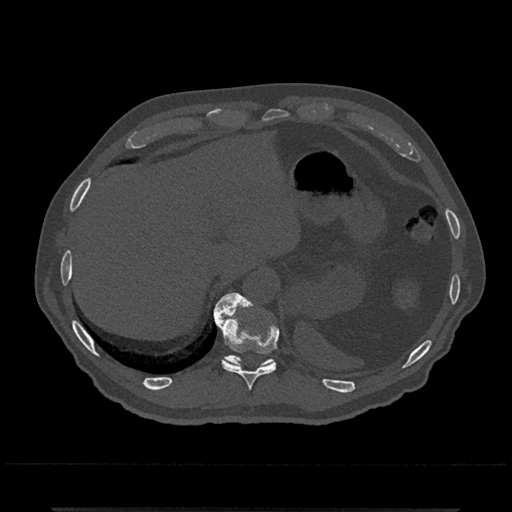
CT including the spine, one axial slice. Slice 537 of 797 in the series (ordered by position). Reconstruction kernel Br40s/3. Bone window (W 1800 / L 400 HU). 0.5 mm slice thickness. 512 × 512 image matrix, field of view 393 × 393 mm. Patient: male, 67 years. Case-level facts recorded for this patient, not image findings: primary cancer: prostate.
Annotated regions visible in this slice (semi-automatically segmented with operator editing):
- T10 vertebra: bounding box [x1, y1, x2, y2] px = [214, 292, 278, 391]
- T11 vertebra: [214, 295, 275, 367]